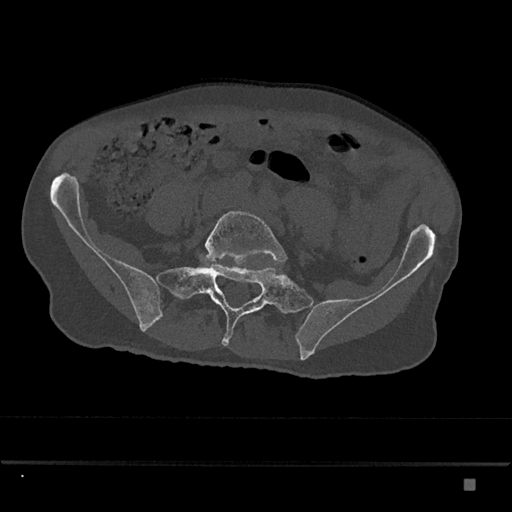
CT including the spine, one axial slice. 120 kVp. Bone window (W 1800 / L 400 HU). 0.5 mm slice thickness. 512 × 512 image matrix, field of view 390 × 390 mm. Patient: male, 72 years. From the clinical record (not read from this slice): primary cancer: prostate.
Annotated regions visible in this slice (semi-automatic segmentation, software-assisted and operator-edited):
- L5 vertebra: bounding box [x1, y1, x2, y2] px = [205, 211, 287, 266]